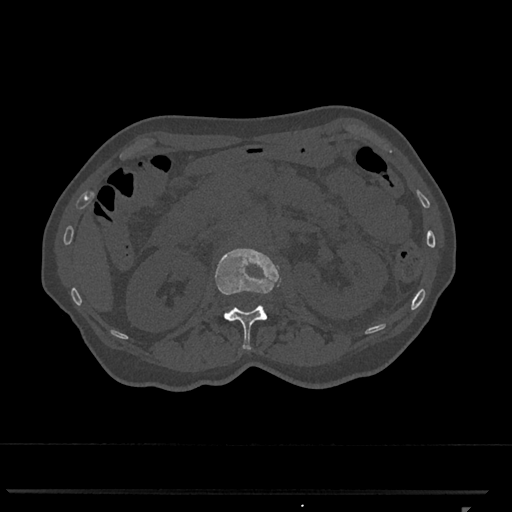
CT including the spine, one axial slice. Position 391 of 793 along the scan axis. Reconstruction kernel Br40s/3. Bone window (W 1800 / L 400 HU). 512 × 512 image matrix. Female patient, age 62 years. Case-level facts recorded for this patient, not image findings: primary cancer: renal.
Outlined on this slice (semi-automatic segmentation, software-assisted and operator-edited):
- L1 vertebra: bounding box [x1, y1, x2, y2] px = [215, 248, 281, 350]